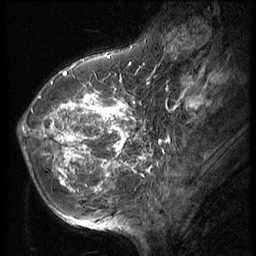
Breast MRI (dynamic contrast-enhanced), one sagittal slice. Slice 19 of 56 in the series (ordered by position). 3 images stored at this slice position (order not interpretable as contrast timing). 1.5 T. TE 4.2 ms, TR 9 ms. 2.5 mm slice thickness. 256 × 256 image matrix. Female patient, age 49 years. Case-level facts recorded for this patient, not image findings: setting: breast cancer imaged before/during neoadjuvant chemotherapy; receptor status: HER2-positive.
Outlined on this slice (semi-automatic segmentation, software-assisted and operator-edited):
- analysis volume of interest (the breast-tissue region the enhancement analysis was run in; not a lesion): box from (x=18, y=79) to (x=138, y=203) px
- tumour enhancement mask (voxels above the 140 % enhancement threshold inside the analysis volume of interest): (x=22, y=82)–(x=137, y=191)